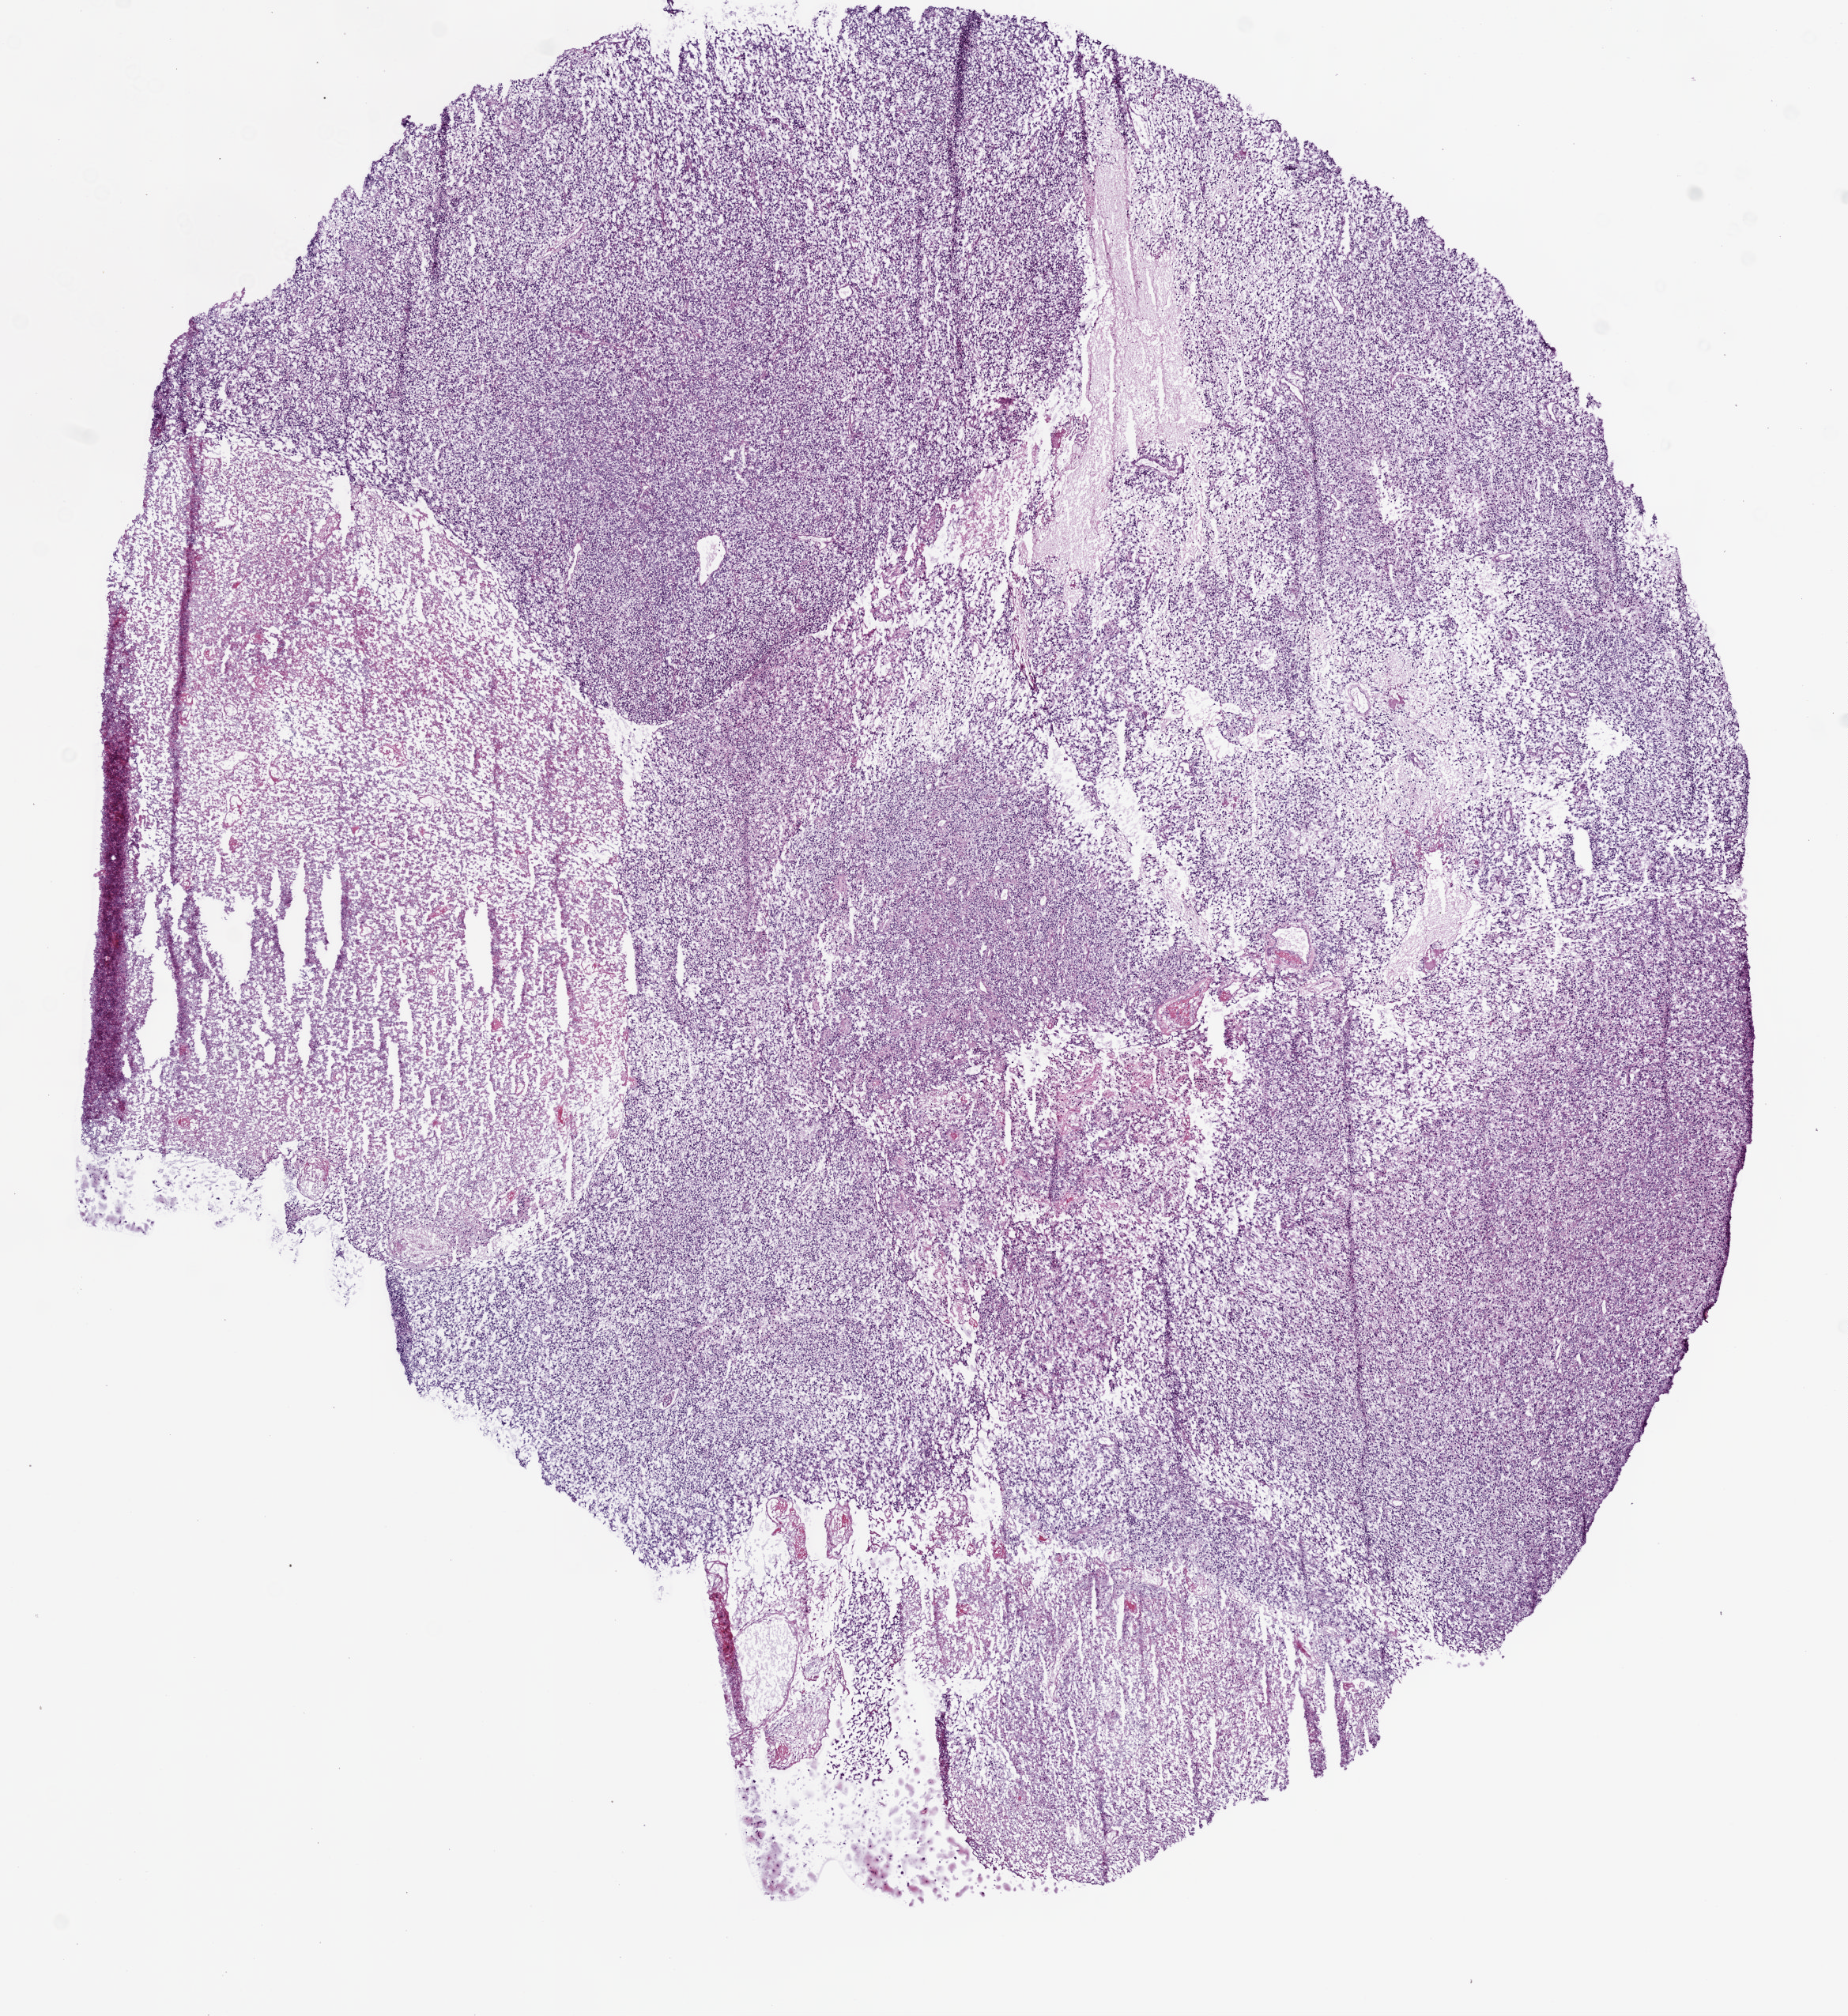
H&E-stained whole-slide image — whole scanned area (about 9.4 x 10.2 mm) shown as a low-resolution overview, frozen section, sample: primary tumour, brain. Female patient; age at initial diagnosis 54 years. Pathologist review of this section (percent, as recorded): tumour cells 85%, tumour nuclei 85%, normal cells 0%, stromal cells 0%, necrosis 15%.
Histologic diagnosis: Glioblastoma.